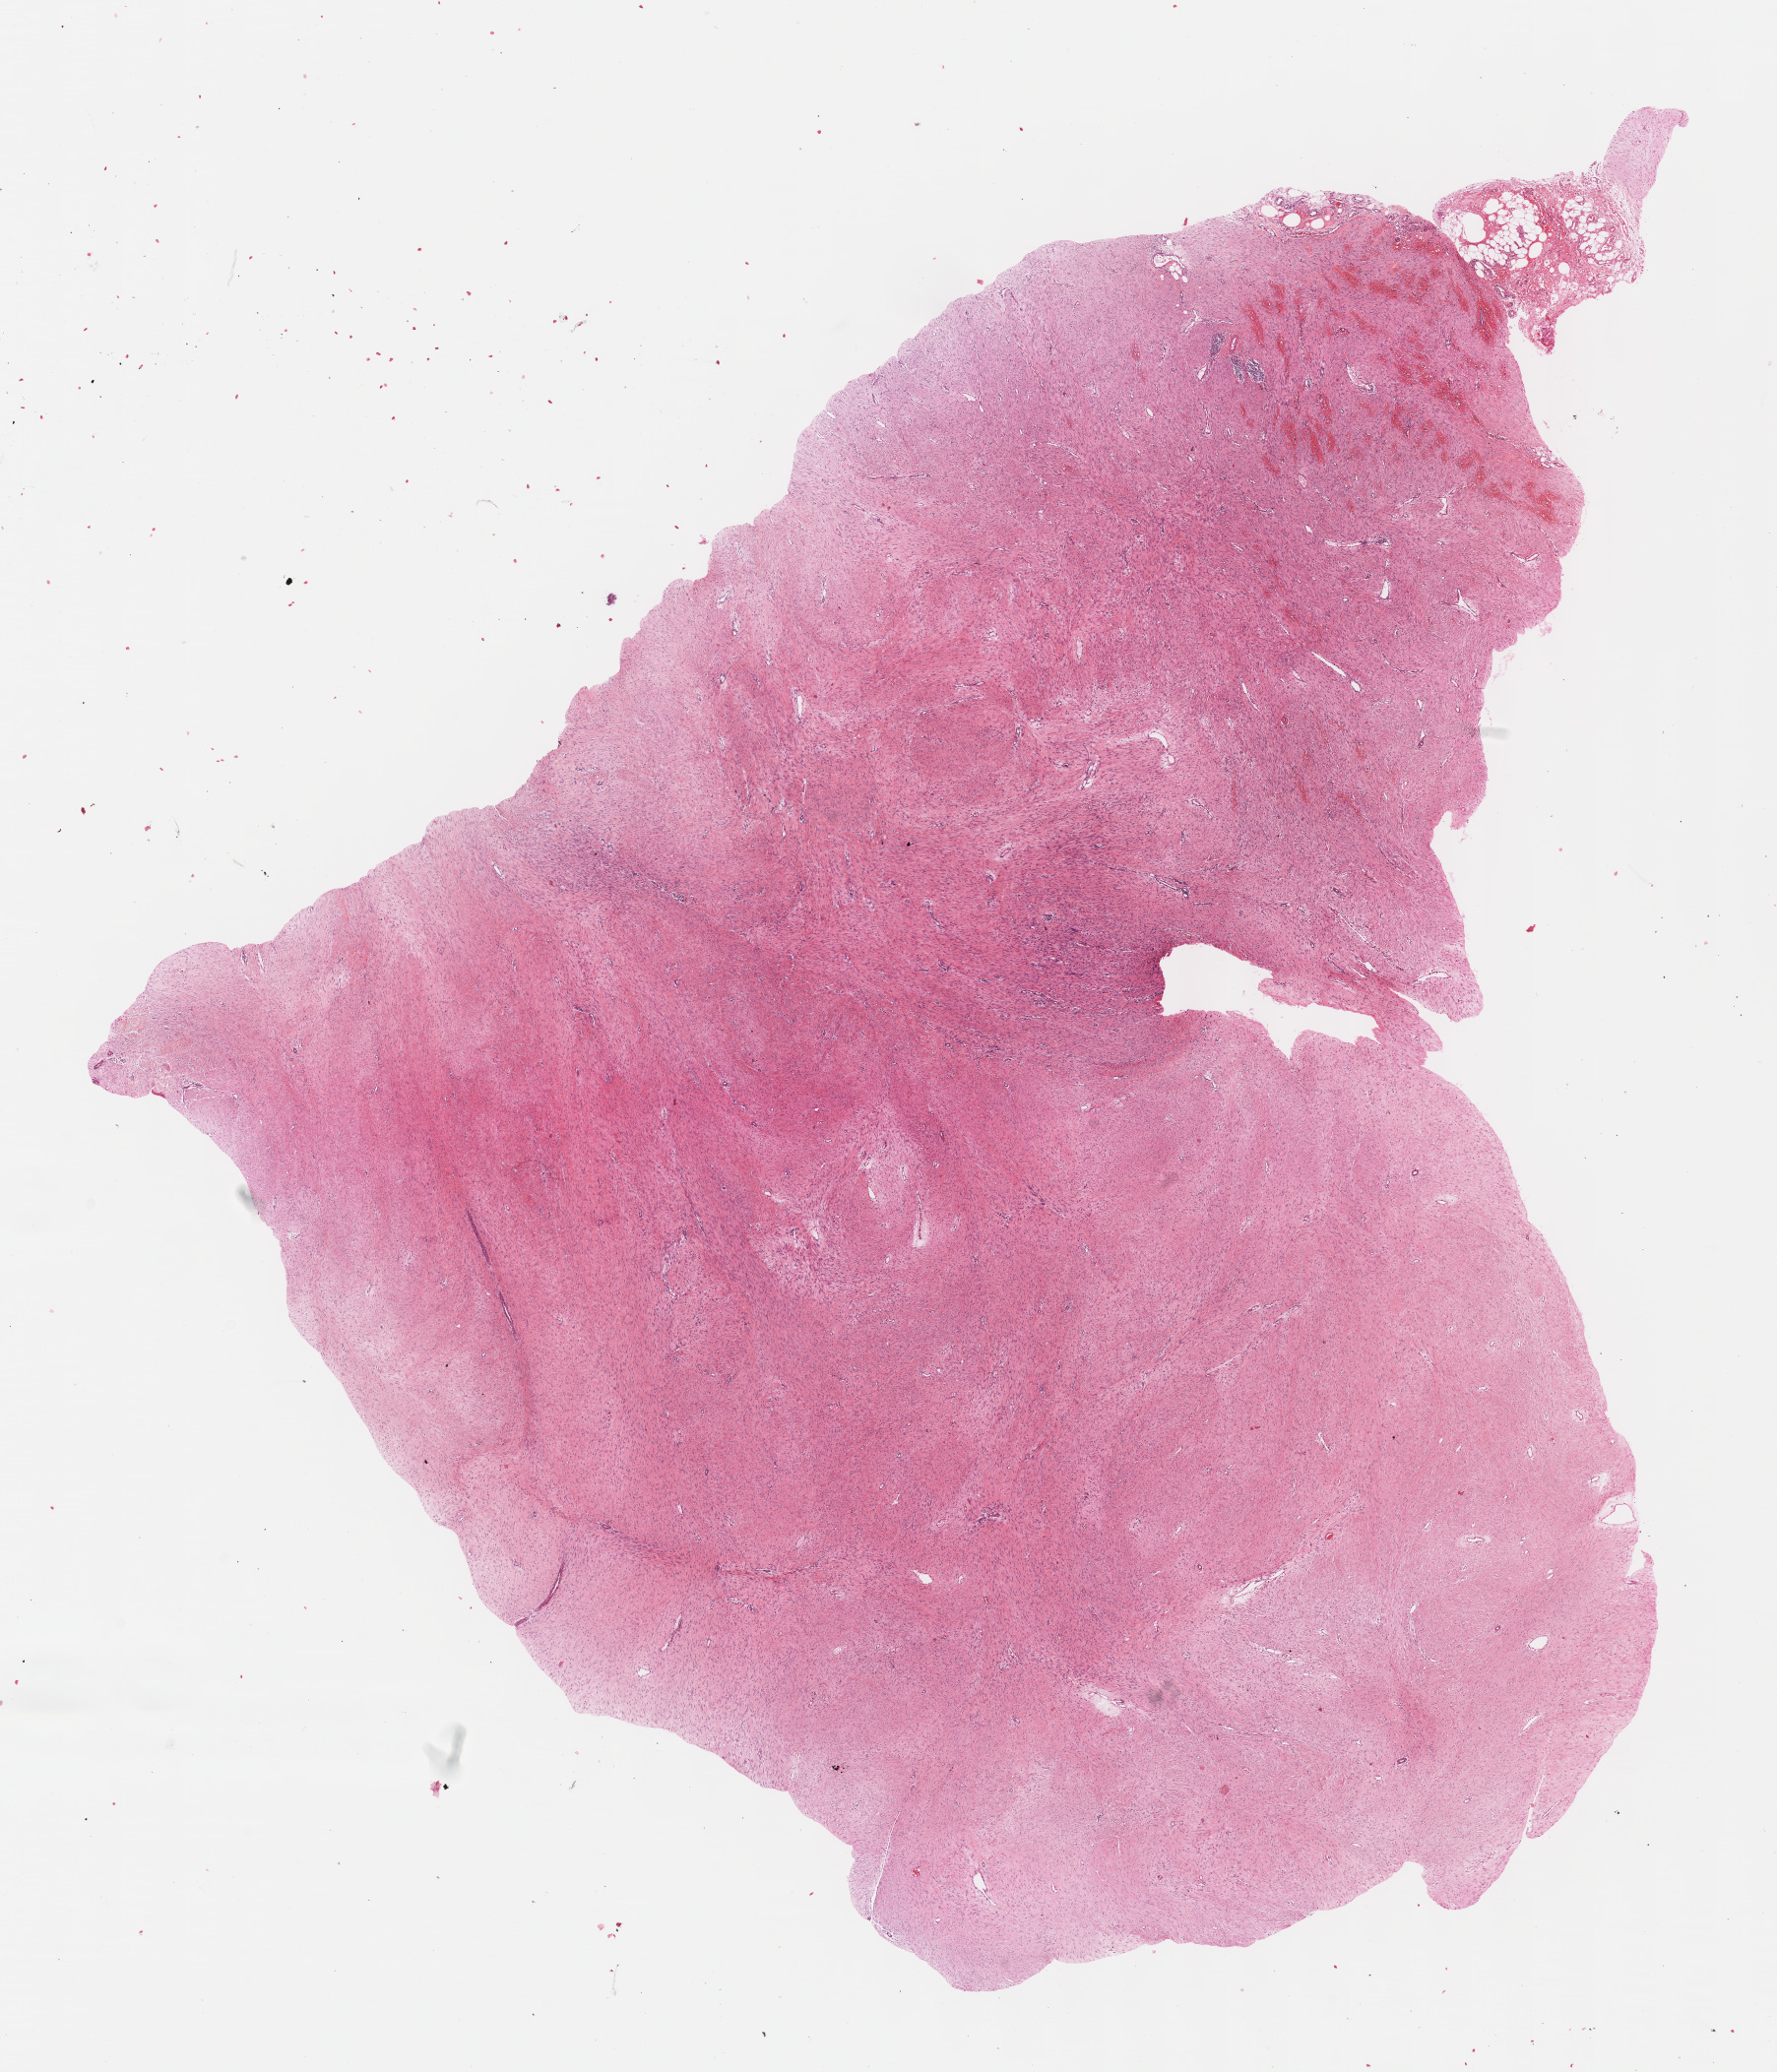
Hematoxylin and eosin (H&E) stained whole-slide image, whole scanned area (about 14.6 x 17.0 mm) shown as a low-resolution overview, formalin-fixed paraffin-embedded (FFPE) diagnostic section, primary tumour sample from the connective, subcutaneous and other soft tissues. Patient: female, age at initial diagnosis 24 years.
* diagnosis: Aggressive fibromatosis